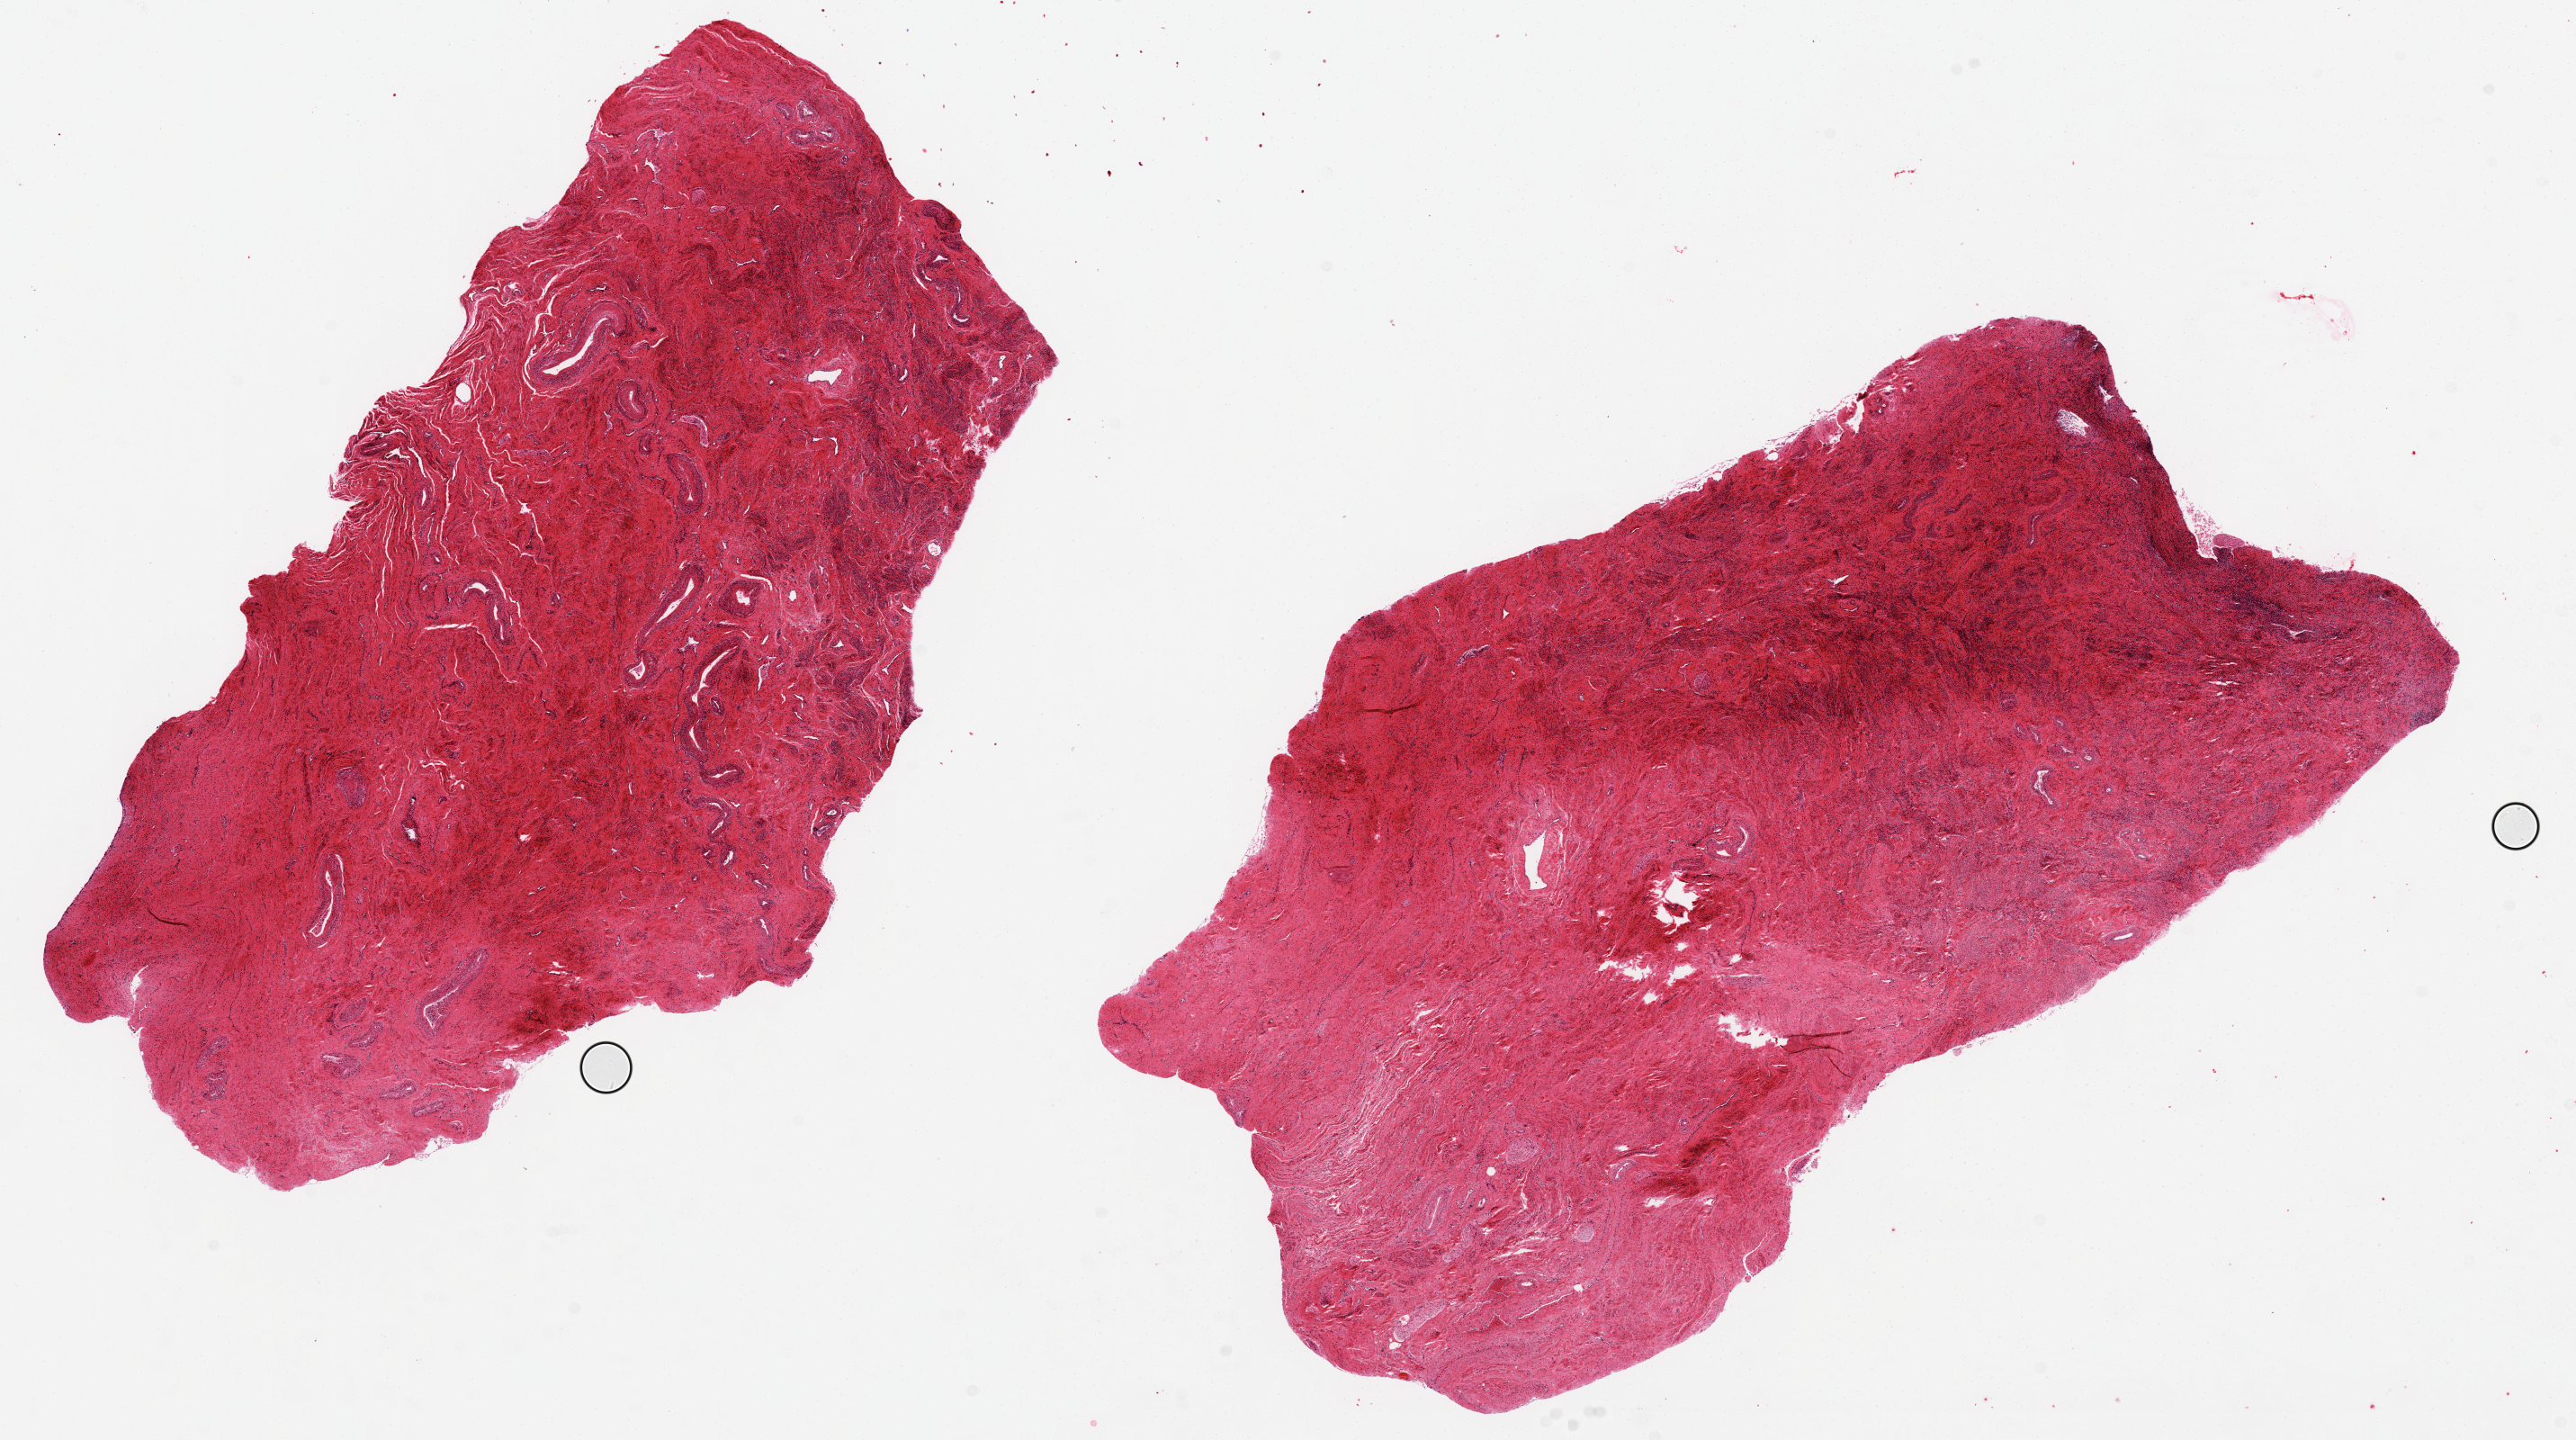
Whole-slide image, haematoxylin and eosin stain — whole scanned area (about 22.6 x 12.7 mm) shown as a low-resolution overview, PAXgene-fixed, paraffin-embedded tissue, target tissue: endocervix, tissue donor sample. Female donor.
Review note (as recorded): No epithelium. 2 pieces: largest.